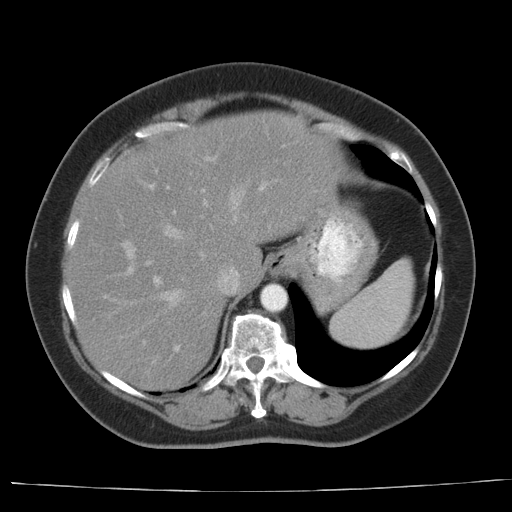
Contrast-enhanced abdominal CT, one axial slice; slice 27 of 44 in the series (ordered by position); reconstruction kernel AA-1; intravenous contrast given; soft-tissue window (W 400 / L 40 HU); 5 mm slice thickness; 512 × 512 image matrix, field of view 373 × 373 mm. Female patient. From the clinical record (not read from this slice): diagnosis: colorectal cancer liver metastases, imaged before liver resection; multiple liver metastases: yes; largest metastasis: 1.8 cm; chemotherapy before resection: yes.
Annotated regions visible in this slice (manually delineated by an expert):
- hepatic veins: bounding box <163,193,239,306> (left, top, right, bottom; pixels)
- liver: <67,114,338,390>
- planned liver remnant (the part of the liver to remain after resection): <99,113,338,285>
- portal vein (with intrahepatic branches): <121,180,269,352>